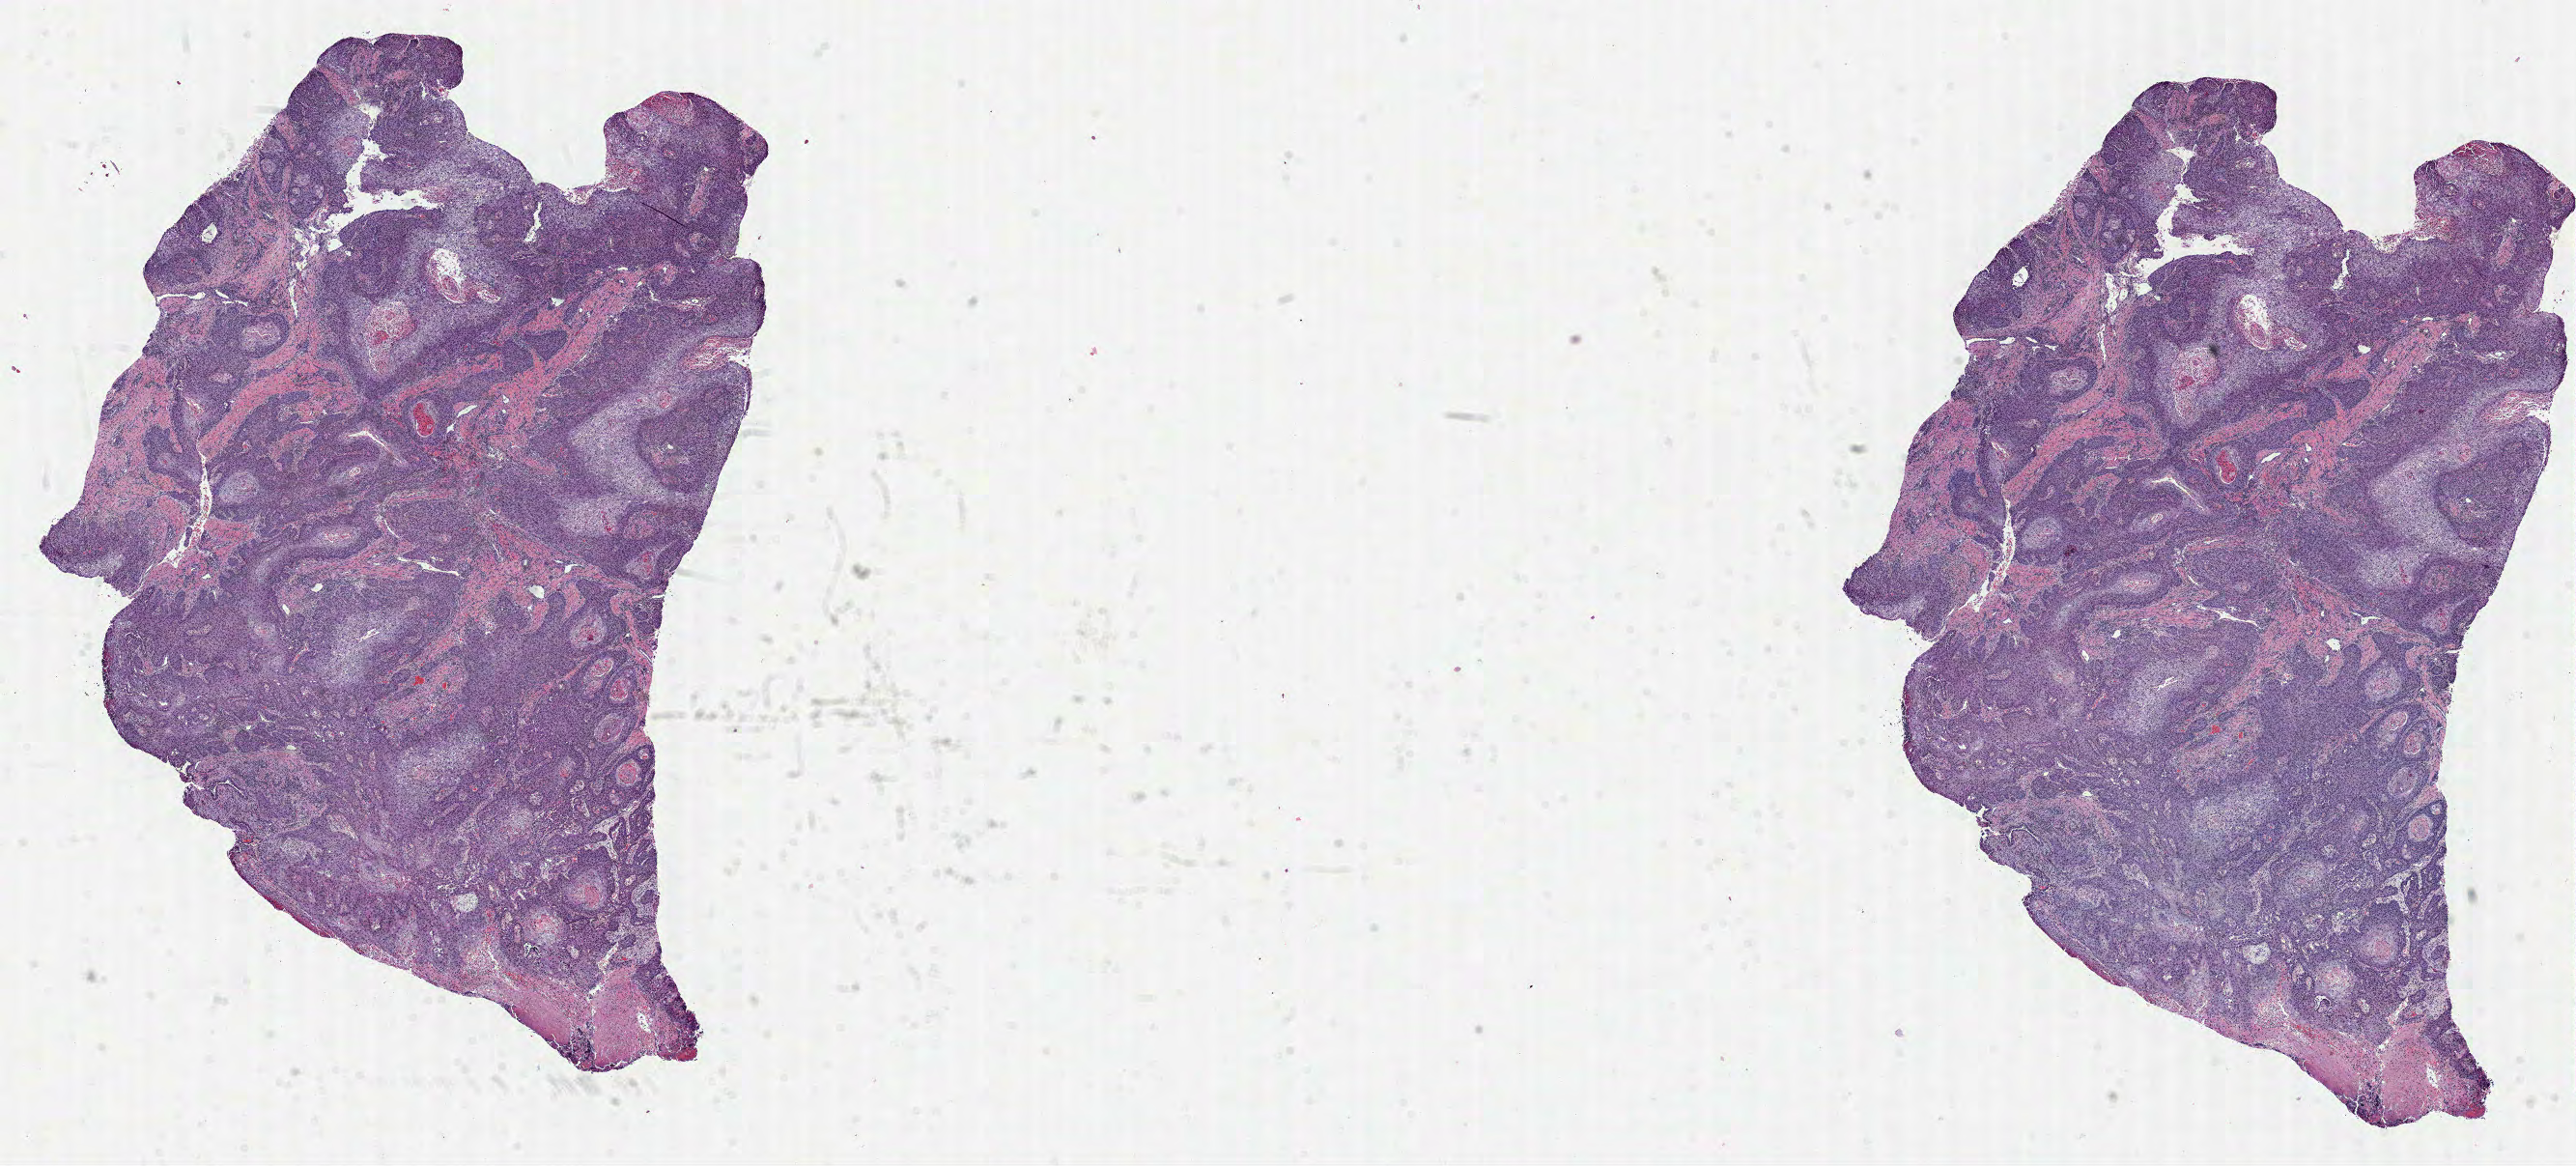
Digitized Hematoxylin and eosin (H&E) stained tissue section (whole slide), shown as a low-resolution overview of the whole scanned area (about 21.5 x 9.7 mm, from a 40x scan), FFPE section, primary tumour sample from the head and neck. Male patient; age at initial diagnosis 56 years. Histologic grade: G2 (moderately differentiated).
Diagnosis: Squamous cell carcinoma, NOS (larynx, NOS). AJCC pathologic stage: III (7th edition).